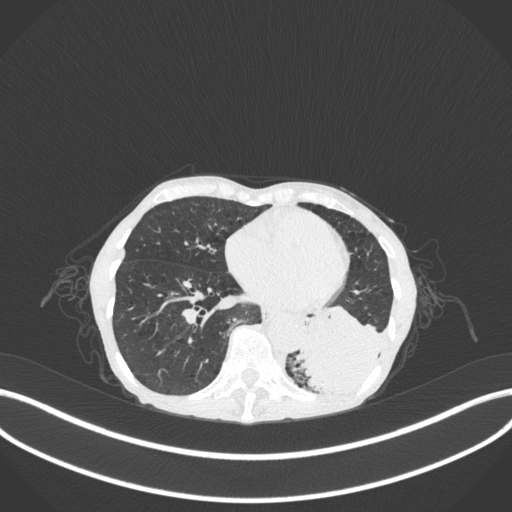
Chest CT, one axial slice. Position 90 of 347 along the scan axis. Reconstruction kernel B31f. Lung window (W 1500 / L -600 HU). 1 mm slice thickness. 512 × 512 image matrix. Patient: female, 70 years. Case-level facts recorded for this patient, not image findings: clinical TNM (as recorded): T3 N0 M0; histopathological grade: G3.
Structures marked on this image (rectangle marked by the reading radiologist):
- lung tumour (recorded histology: small cell carcinoma): bounding box <289,298,394,399> (left, top, right, bottom; pixels)